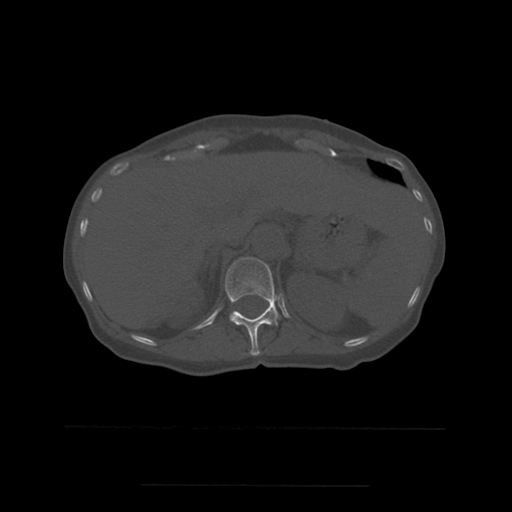
CT including the spine, one axial slice. Slice 257 of 544 in the series (ordered by position). Bone window (W 1800 / L 400 HU). 1.25 mm slice thickness. 512 × 512 image matrix, field of view 350 × 350 mm. Patient age 58 years. Case-level facts recorded for this patient, not image findings: primary cancer: lung.
Structures marked on this image (semi-automatically segmented with operator editing):
- T12 vertebra: bounding box <226,258,279,356> (left, top, right, bottom; pixels)